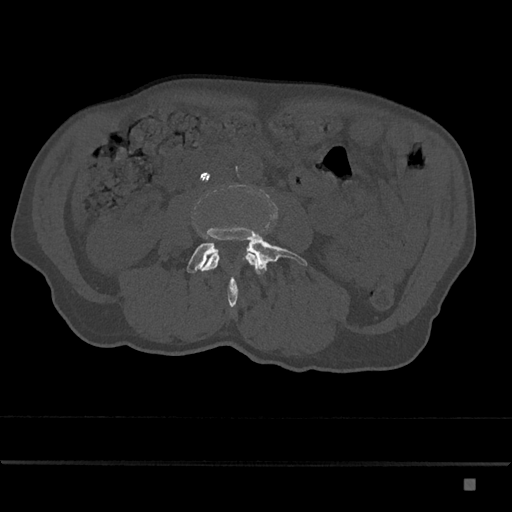
CT including the spine, one axial slice. Position 364 of 797 along the scan axis. Bone window (W 1800 / L 400 HU). 512 × 512 image matrix, field of view 390 × 390 mm. Male patient, age 72 years. From the clinical record (not read from this slice): primary cancer: prostate.
Outlined on this slice (semi-automatically segmented with operator editing):
- L3 vertebra: bounding box (x1, y1, x2, y2) in pixels: (202, 253, 258, 271)
- L4 vertebra: (187, 181, 307, 307)